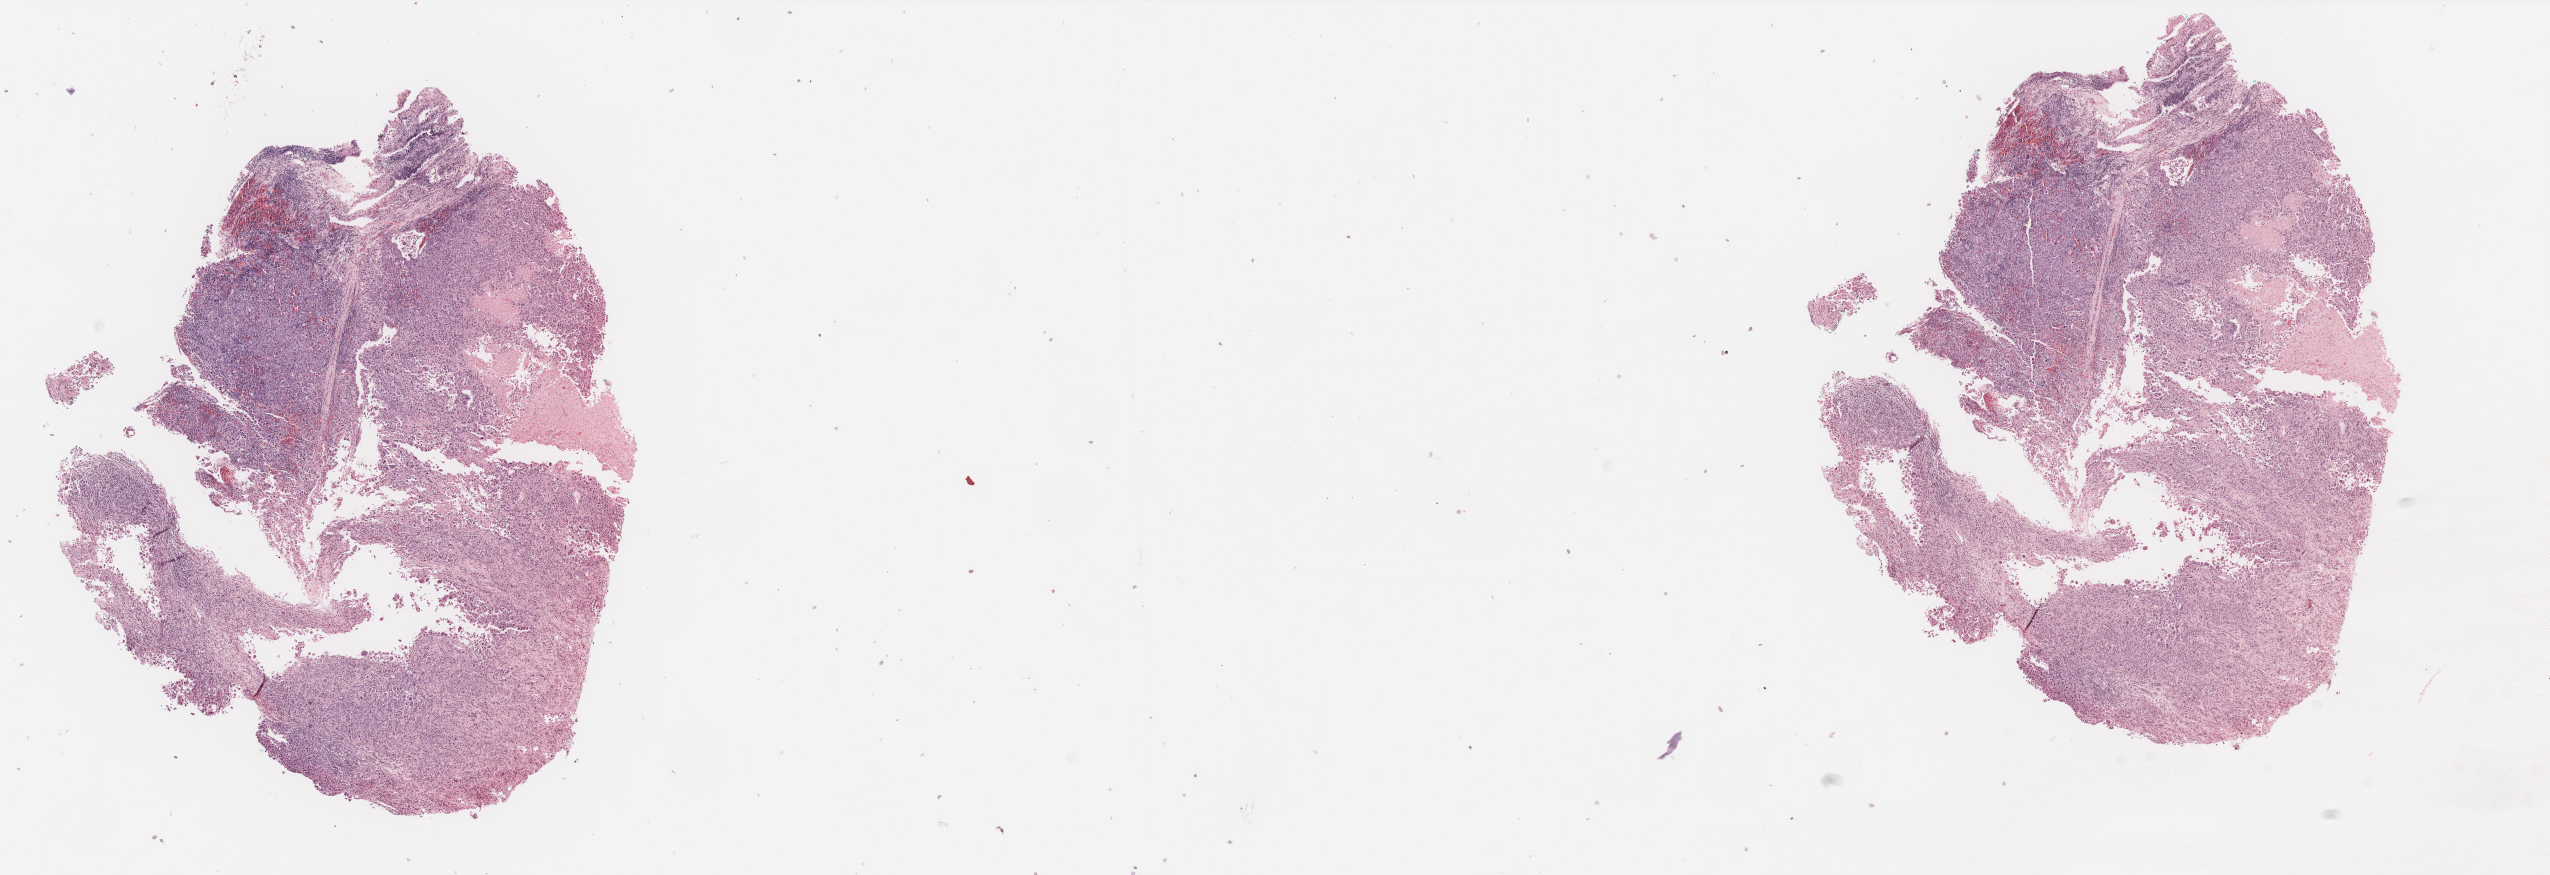
H&E whole-slide image — shown as a low-resolution overview of the whole scanned area (about 20.4 x 7.0 mm); formalin-fixed paraffin-embedded (FFPE) diagnostic section; sample: primary tumour, skin. Patient: female, age at initial diagnosis 37 years.
Pathologic diagnosis: Malignant melanoma, NOS.